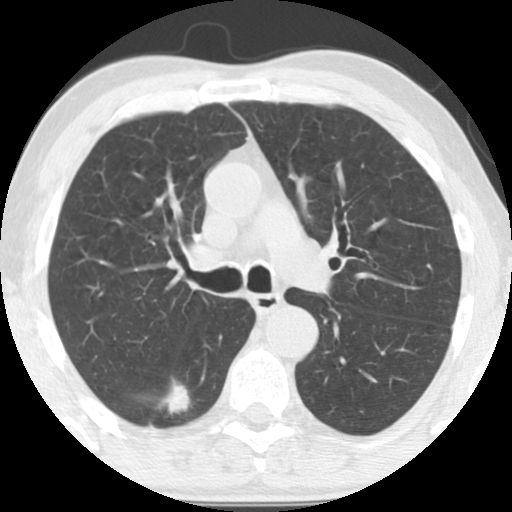
Axial slice from a low-dose chest CT screening exam. Baseline annual screen. Lung window (W 1500 / L -600 HU). 2.5 mm slice thickness. Standard (soft-tissue) reconstruction kernel (STANDARD). 120 kVp. Male, age 64 years at enrolment.
Expert reader's lesion annotation, box from (x=120, y=365) to (x=196, y=433) px. Reader record for this screening exam (exam-level; its link to the box is not recorded): non-calcified nodule or mass ≥4 mm, right lower lobe, 36 × 26 mm, spiculated (stellate) margins, soft tissue attenuation. Official screen result: positive, change unspecified: nodule(s) >= 4 mm or enlarging nodule(s), mass(es), or other non-specific abnormalities suspicious for lung cancer. Later outcome: lung cancer diagnosed 20 days after this screen — adenocarcinoma, NOS, right lower lobe, moderately differentiated (G2), stage IA (AJCC 6th edition), 28 mm at pathology.